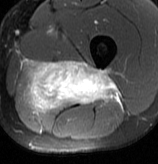
MRI of an extremity soft-tissue mass, one axial slice; slice 43 of 70 in the series (ordered by position); T2-weighted fat-saturated; MR volume resampled by the dataset authors to the PET/CT grid (not the native acquisition matrix); 158 × 164 image matrix, field of view 154 × 160 mm. Male patient. Case-level facts recorded for this patient, not image findings: histological type: extraskeletal osteosarcoma; grade: high; site of the primary tumour: left adductur.
Outlined on this slice (expert contour drawn on MRI and transferred to this co-registered scan by the dataset authors):
- gross tumour volume (mass): bounding box (x1, y1, x2, y2) in pixels: (24, 60, 121, 113)